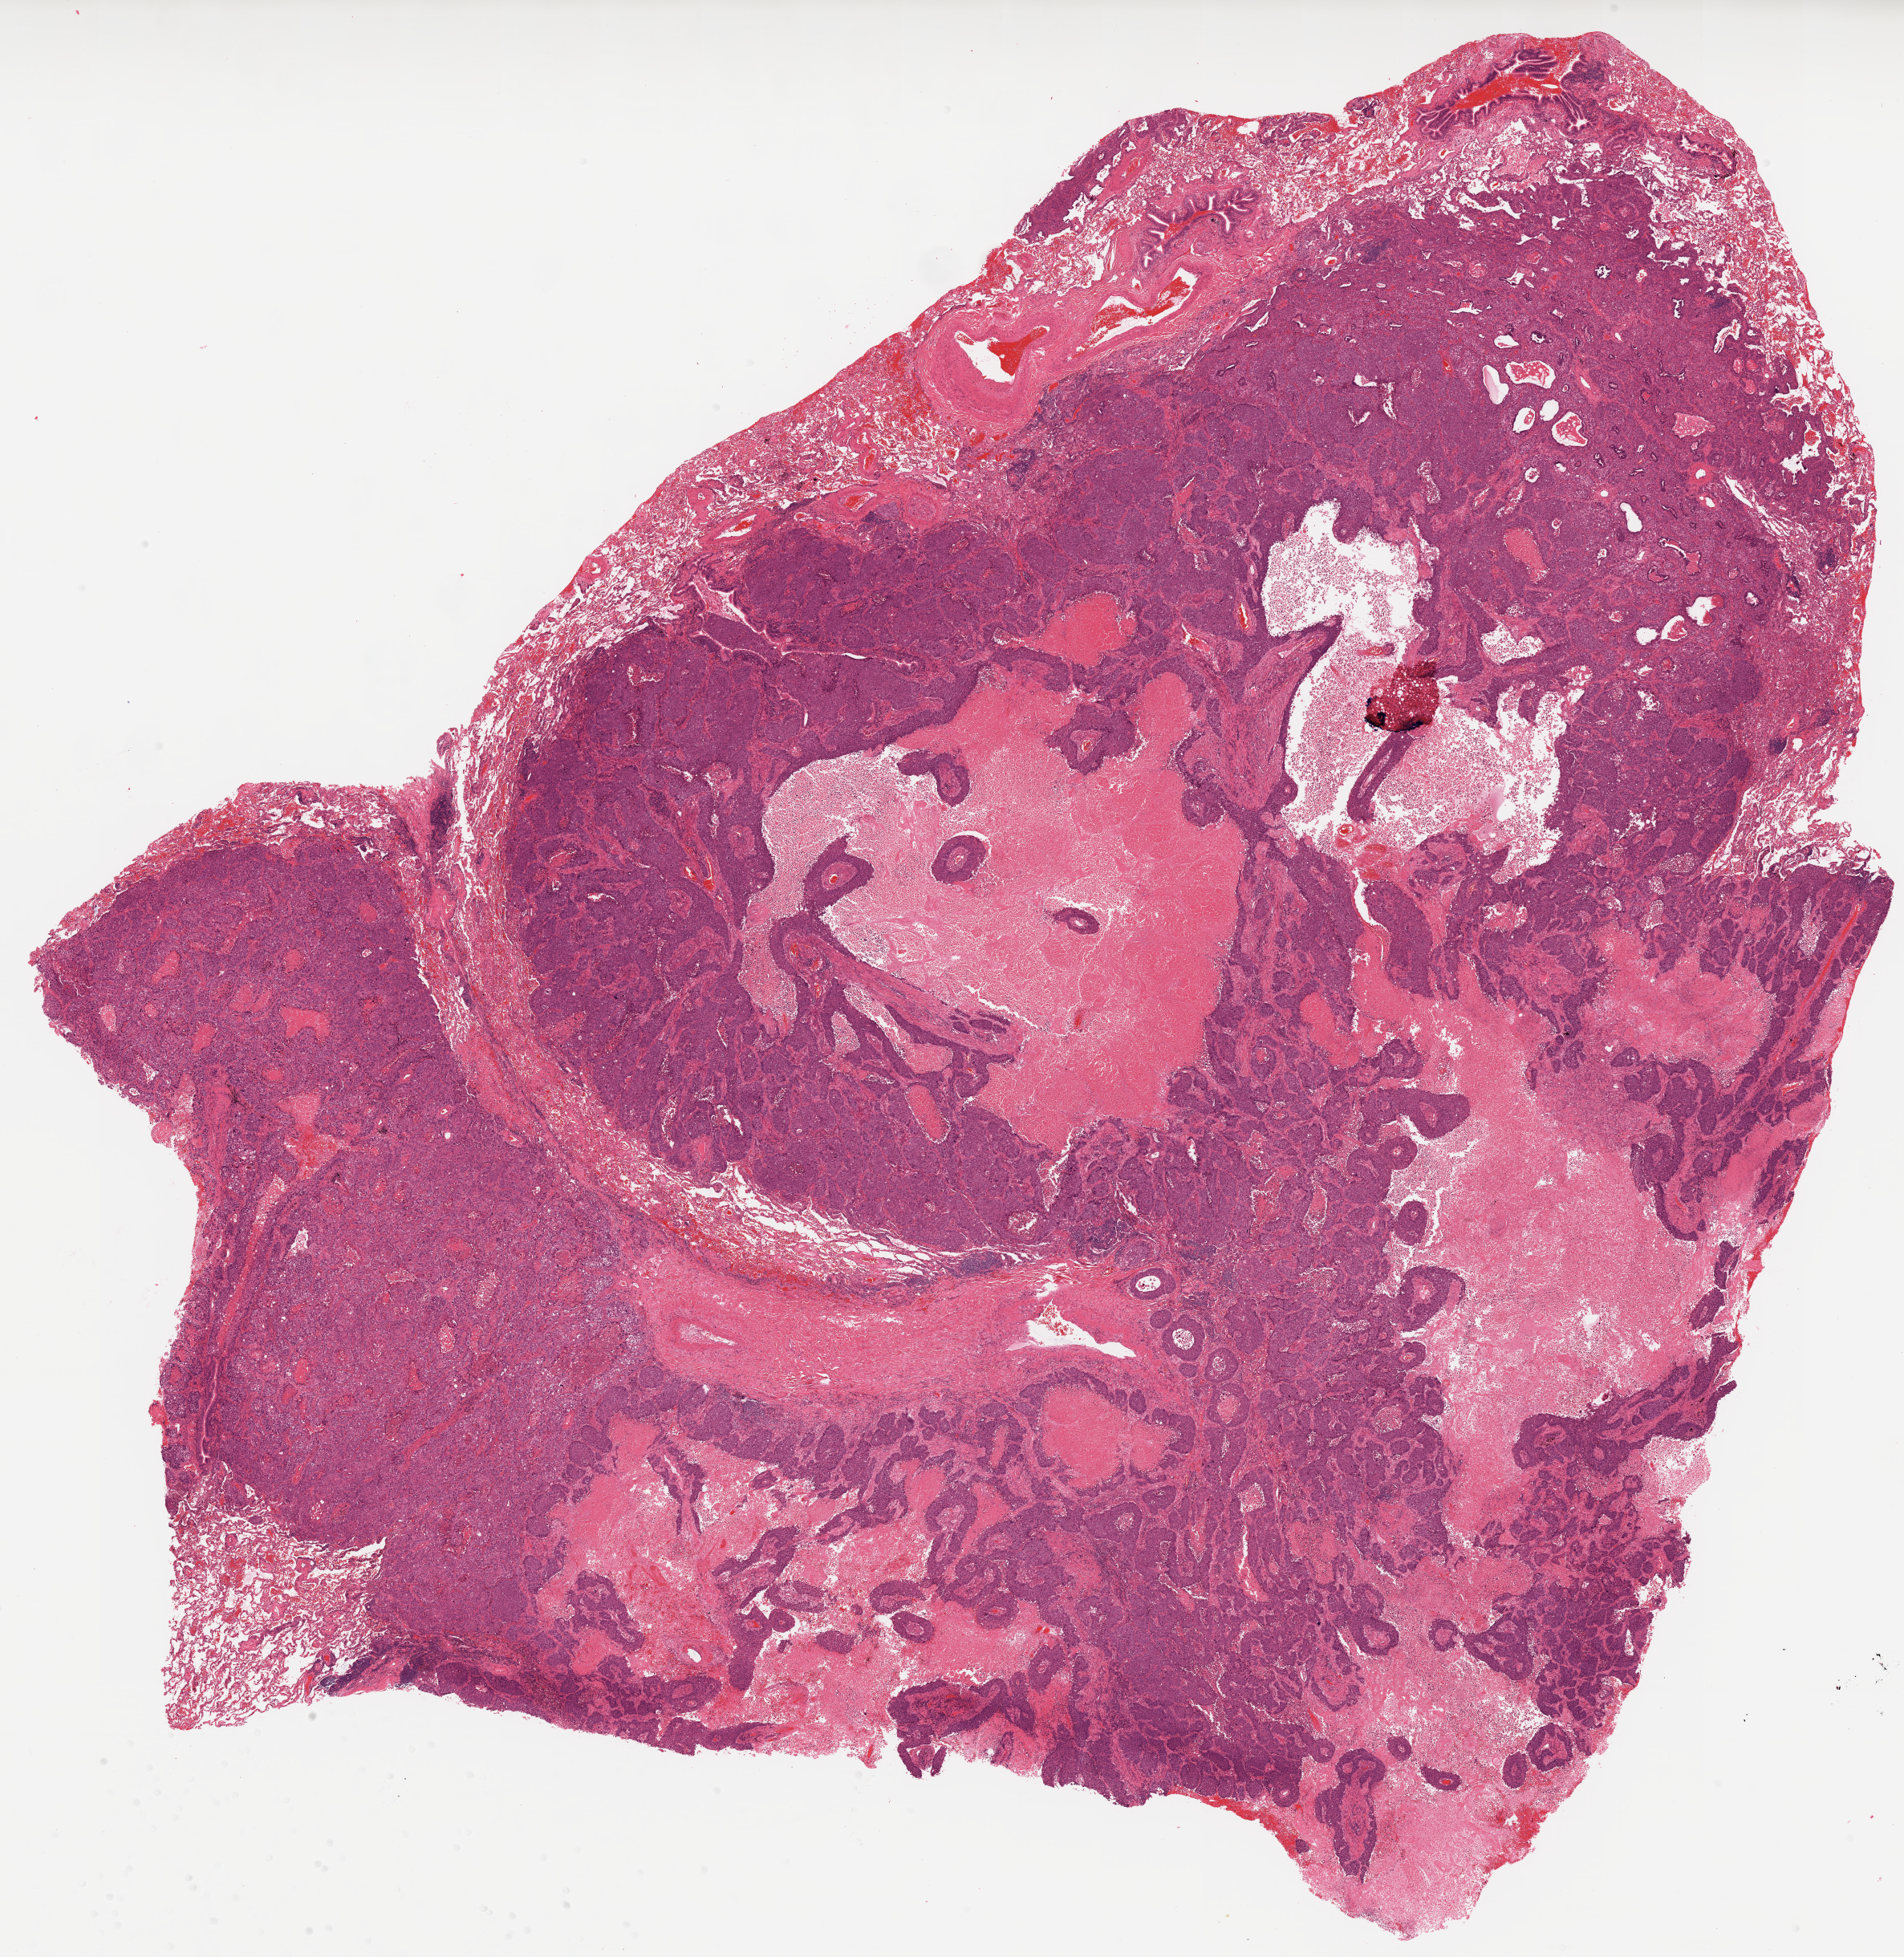
Whole-slide histology image, Hematoxylin and eosin (H&E) stained, whole scanned area (about 19.0 x 19.5 mm, slide scanned at 20x) shown as a low-resolution overview, formalin-fixed paraffin-embedded (FFPE) diagnostic section, primary tumour sample from the lung. Patient: male, age at initial diagnosis 62 years.
* laterality: left
* TNM: T2 N0 M0
* diagnosis: Squamous cell carcinoma, NOS (upper lobe, lung)
* AJCC pathologic stage: IB (6th edition)